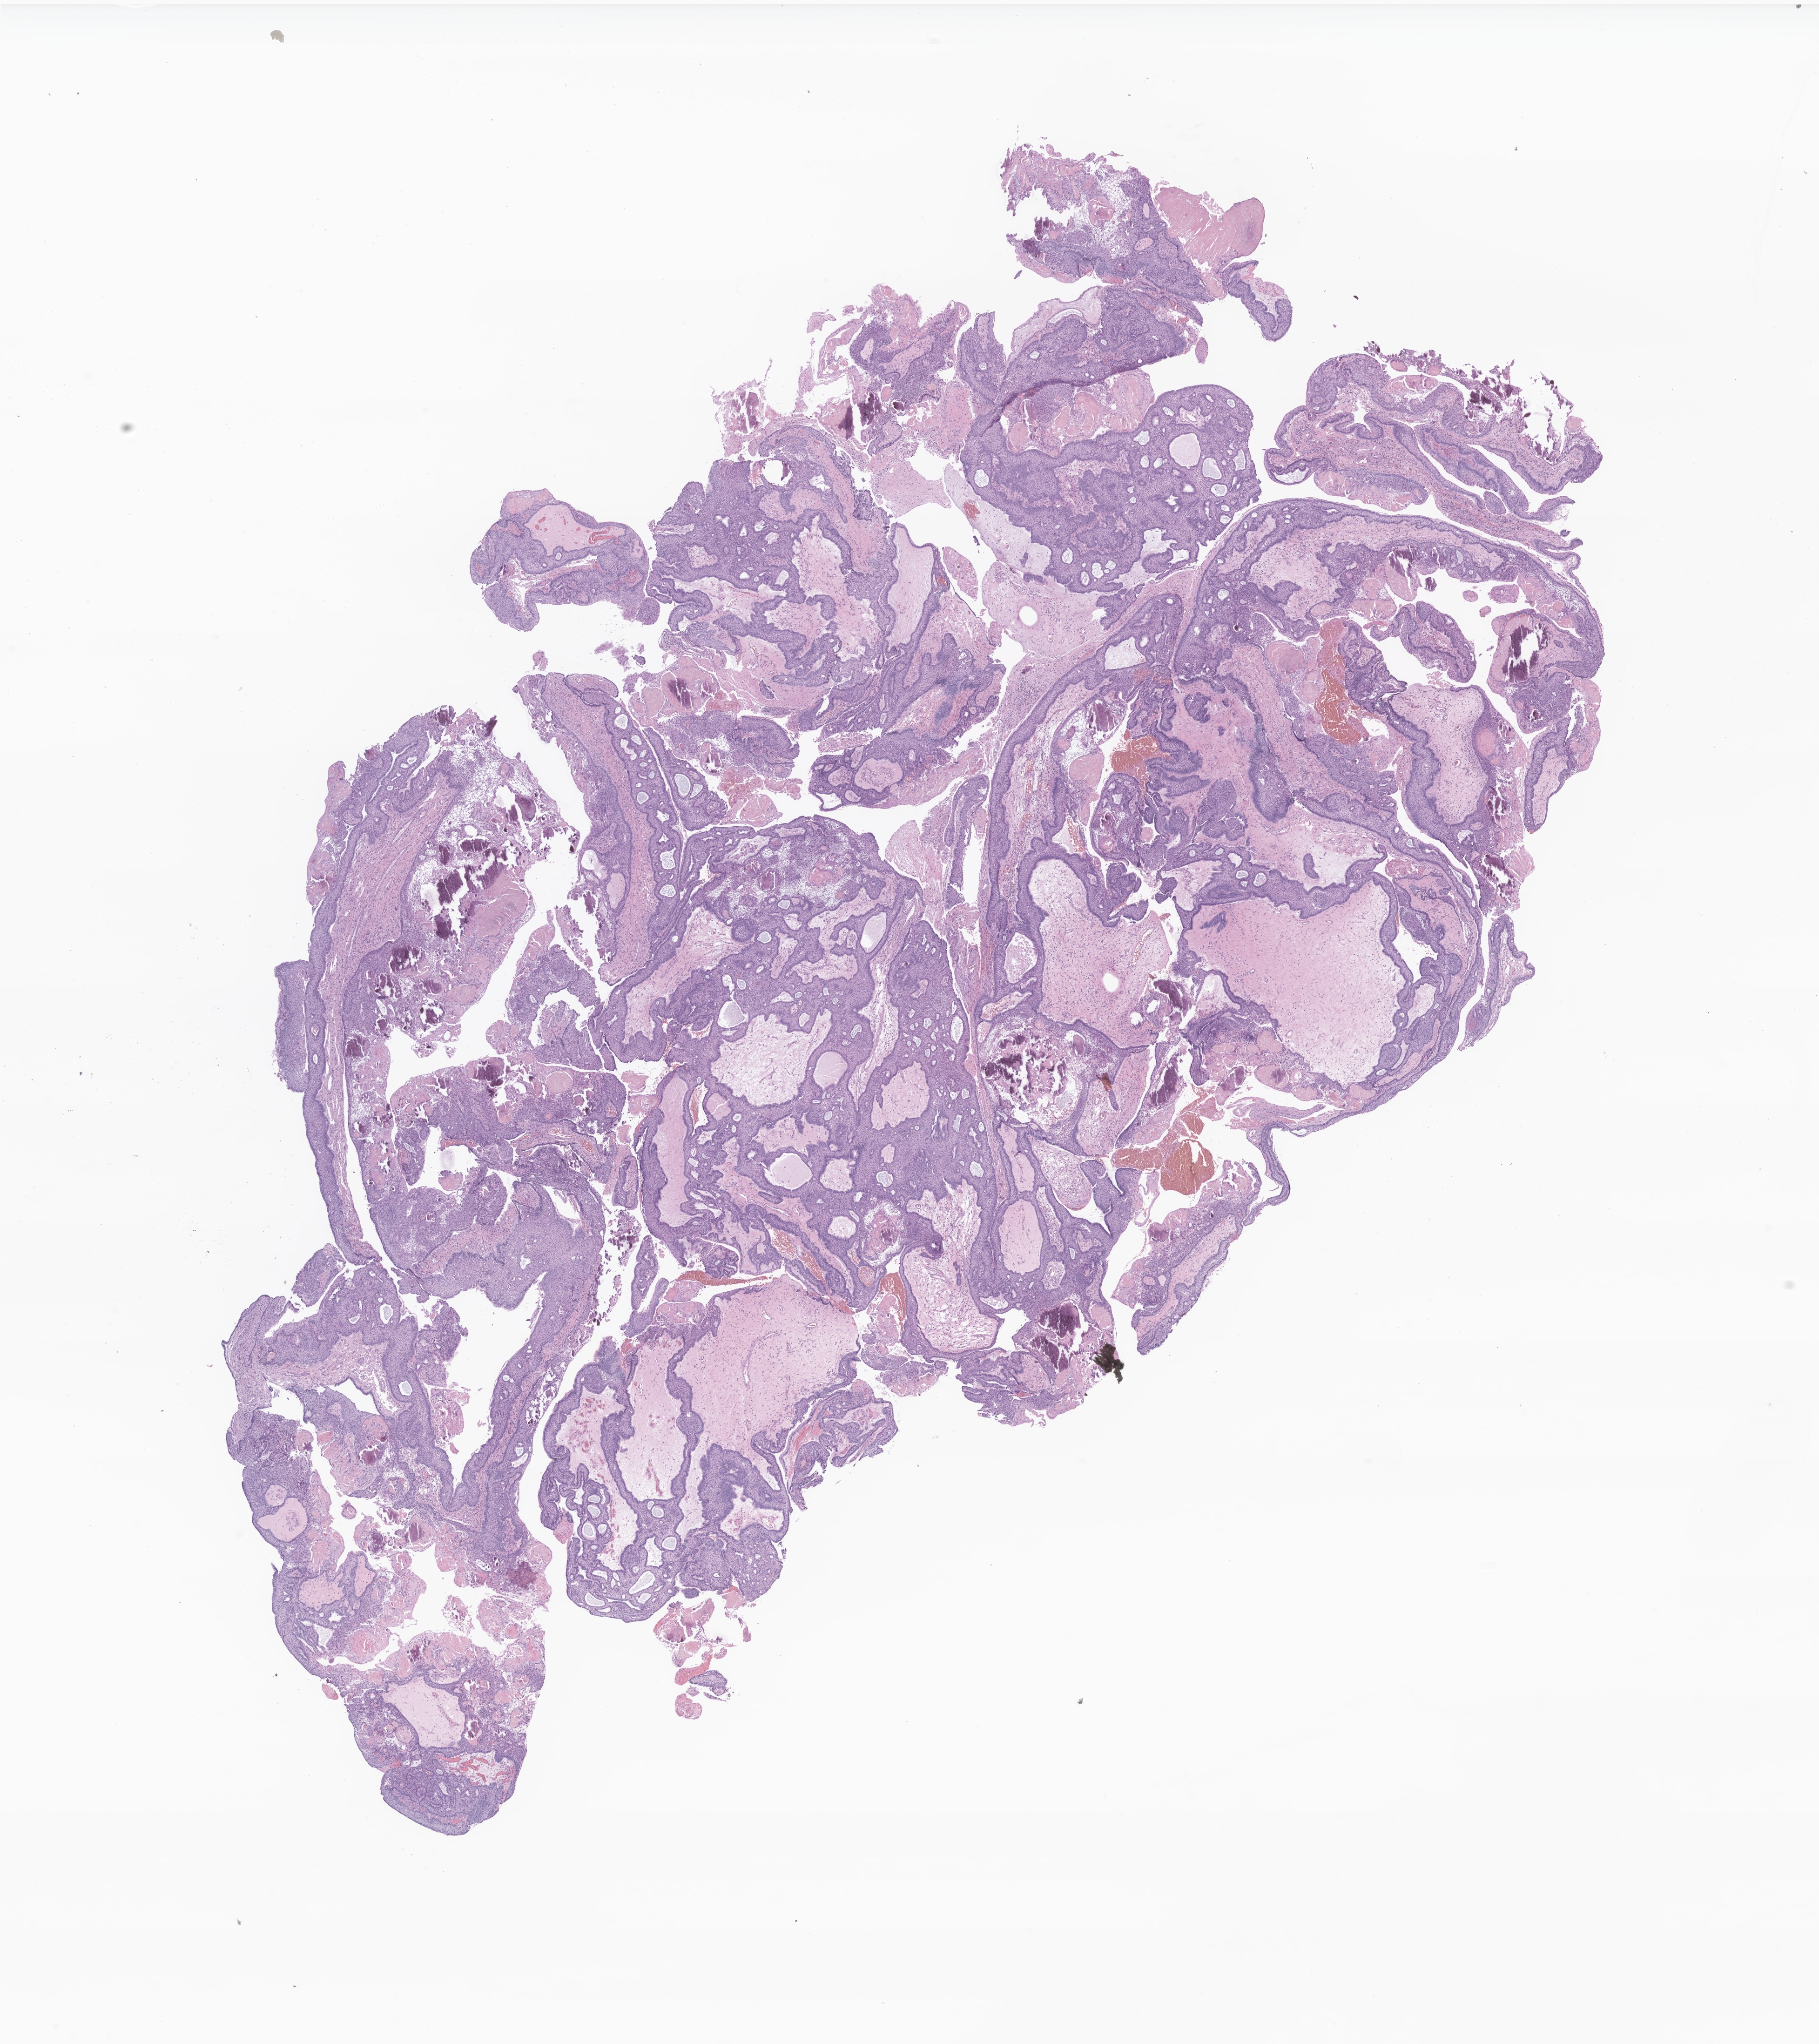
Haematoxylin and eosin whole-slide image of tumor tissue from the brain — low-resolution overview of the scanned area, about 16.5 x 18.5 mm. Formalin-fixed, paraffin-embedded (FFPE) tissue. Patient: male, age 145 months.
• diagnosis: Craniopharyngioma, adamantinomatous